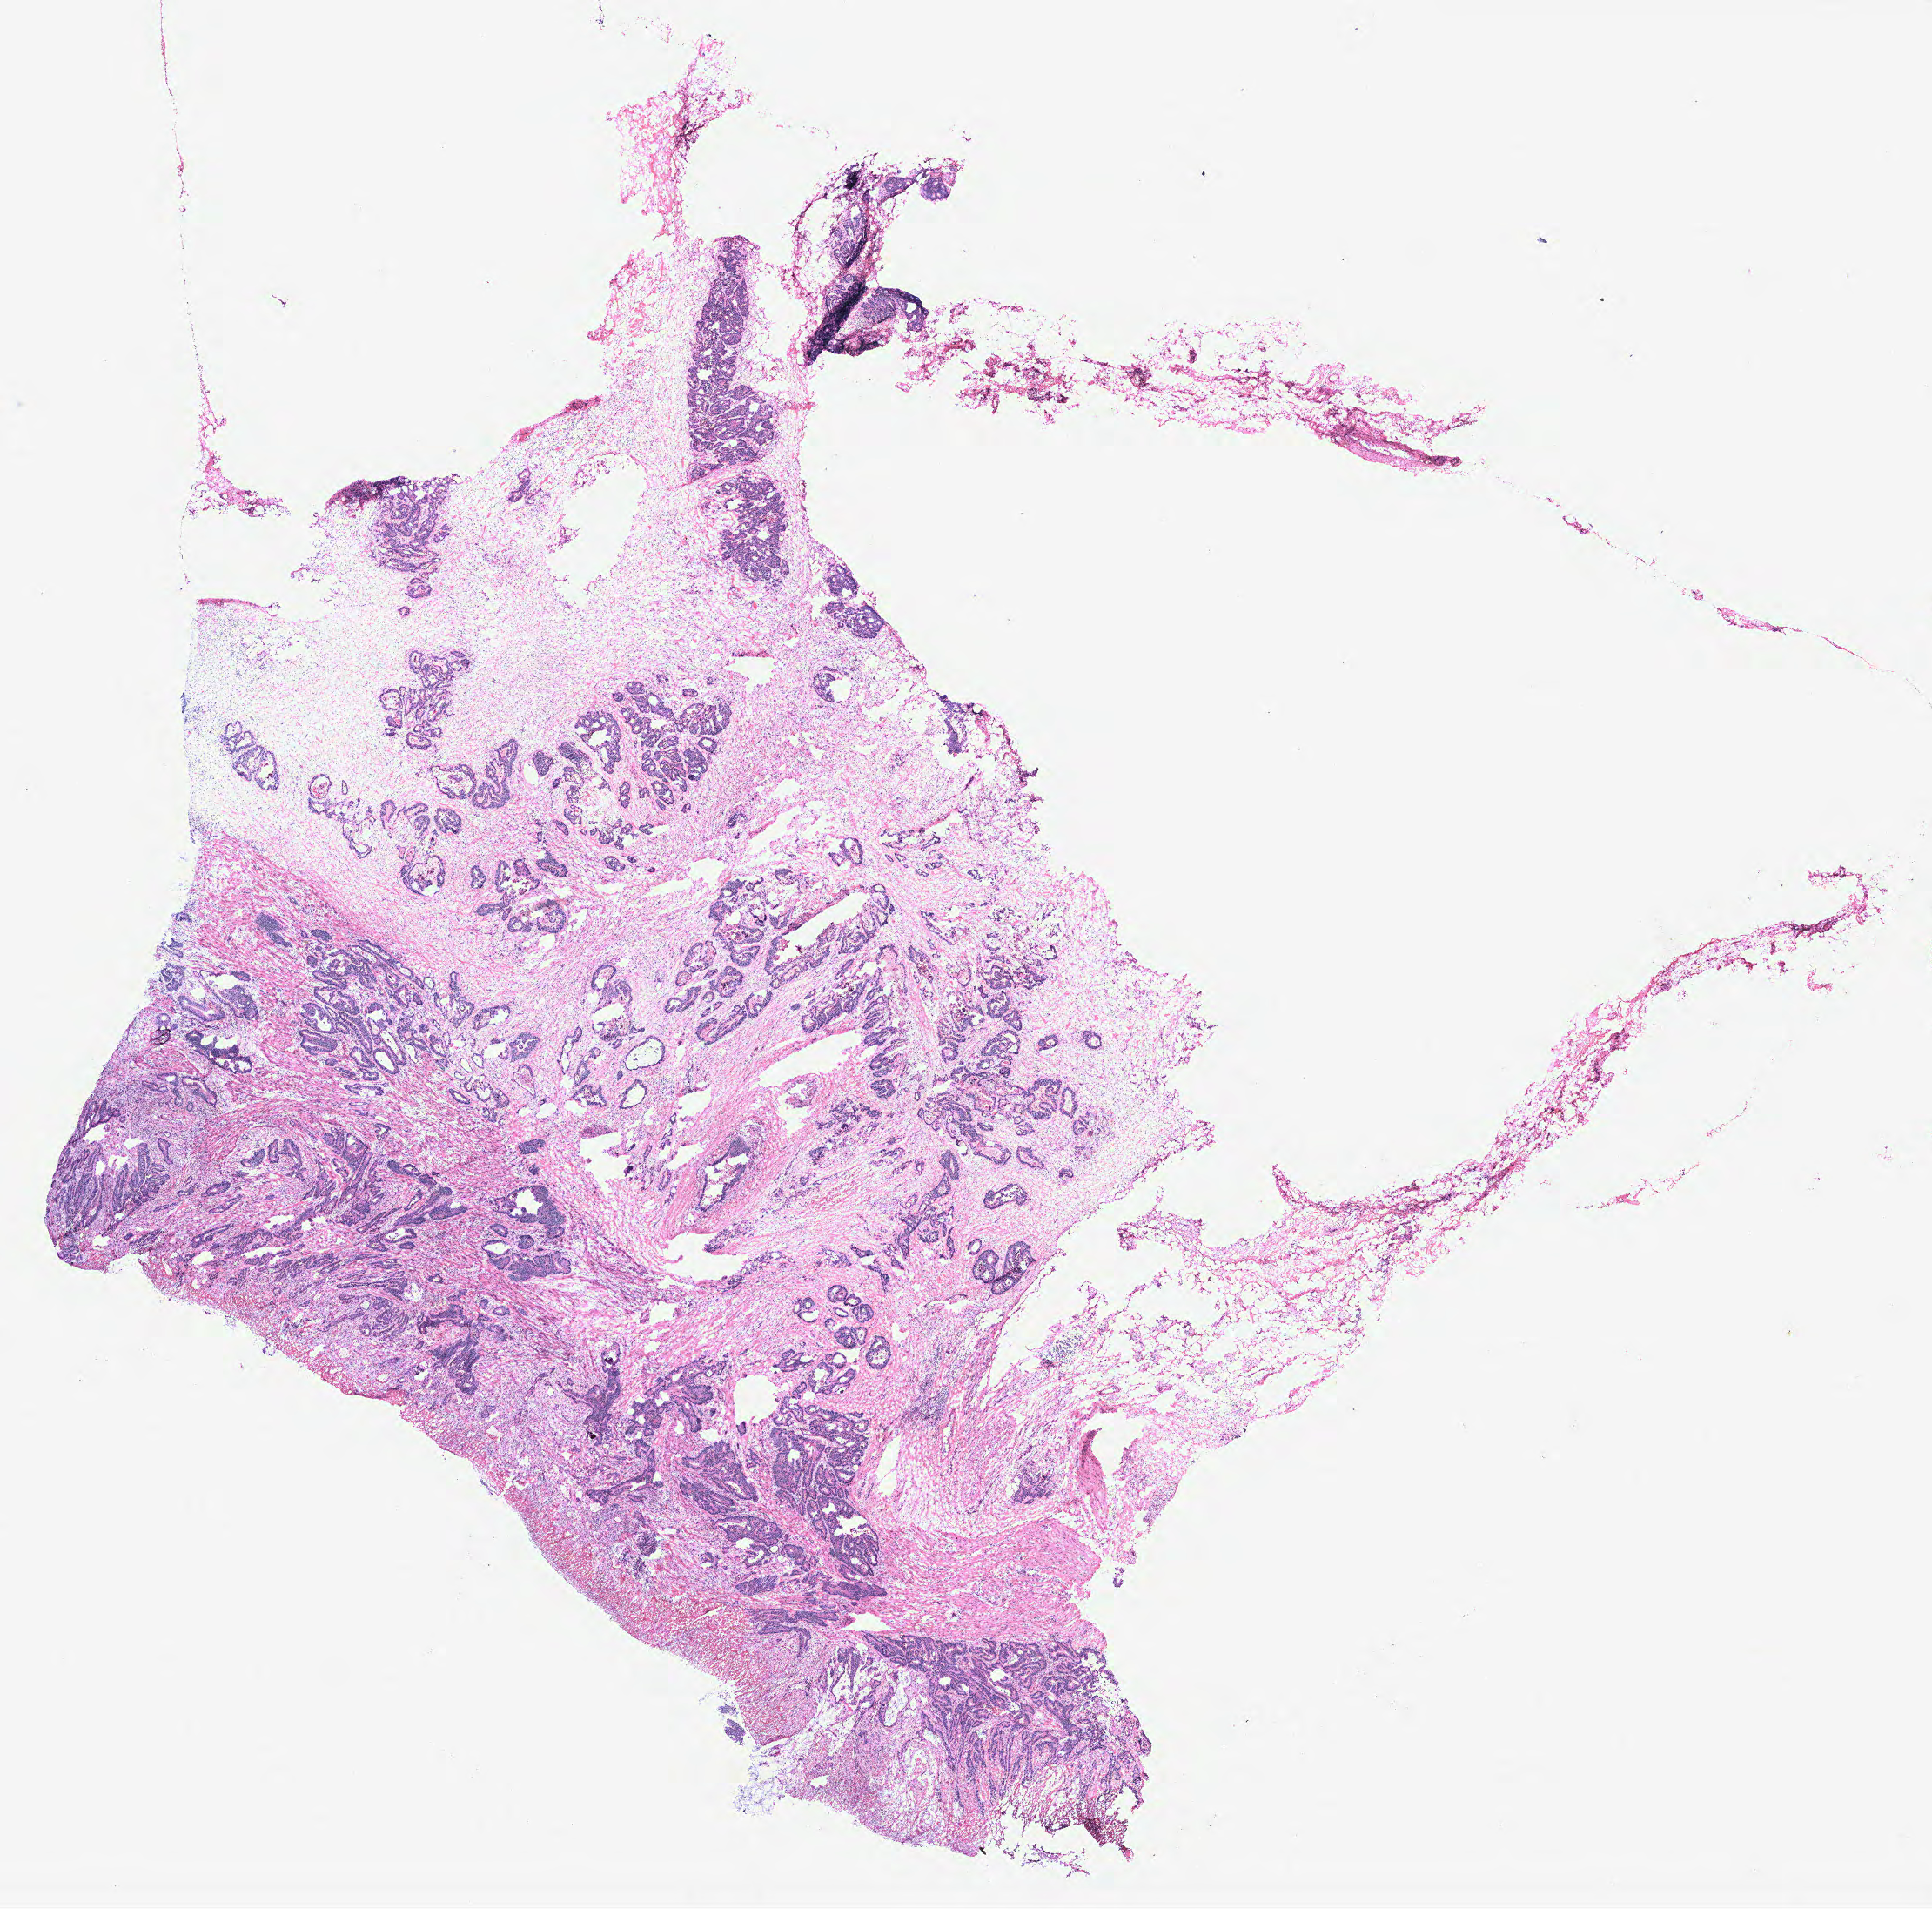
Whole-slide histology image, H&E-stained, low-resolution overview of the scanned area, about 17.8 x 17.6 mm. Colon, tissue type not recorded.
Patient diagnosis (cohort enrolment): colon cancer (colon).